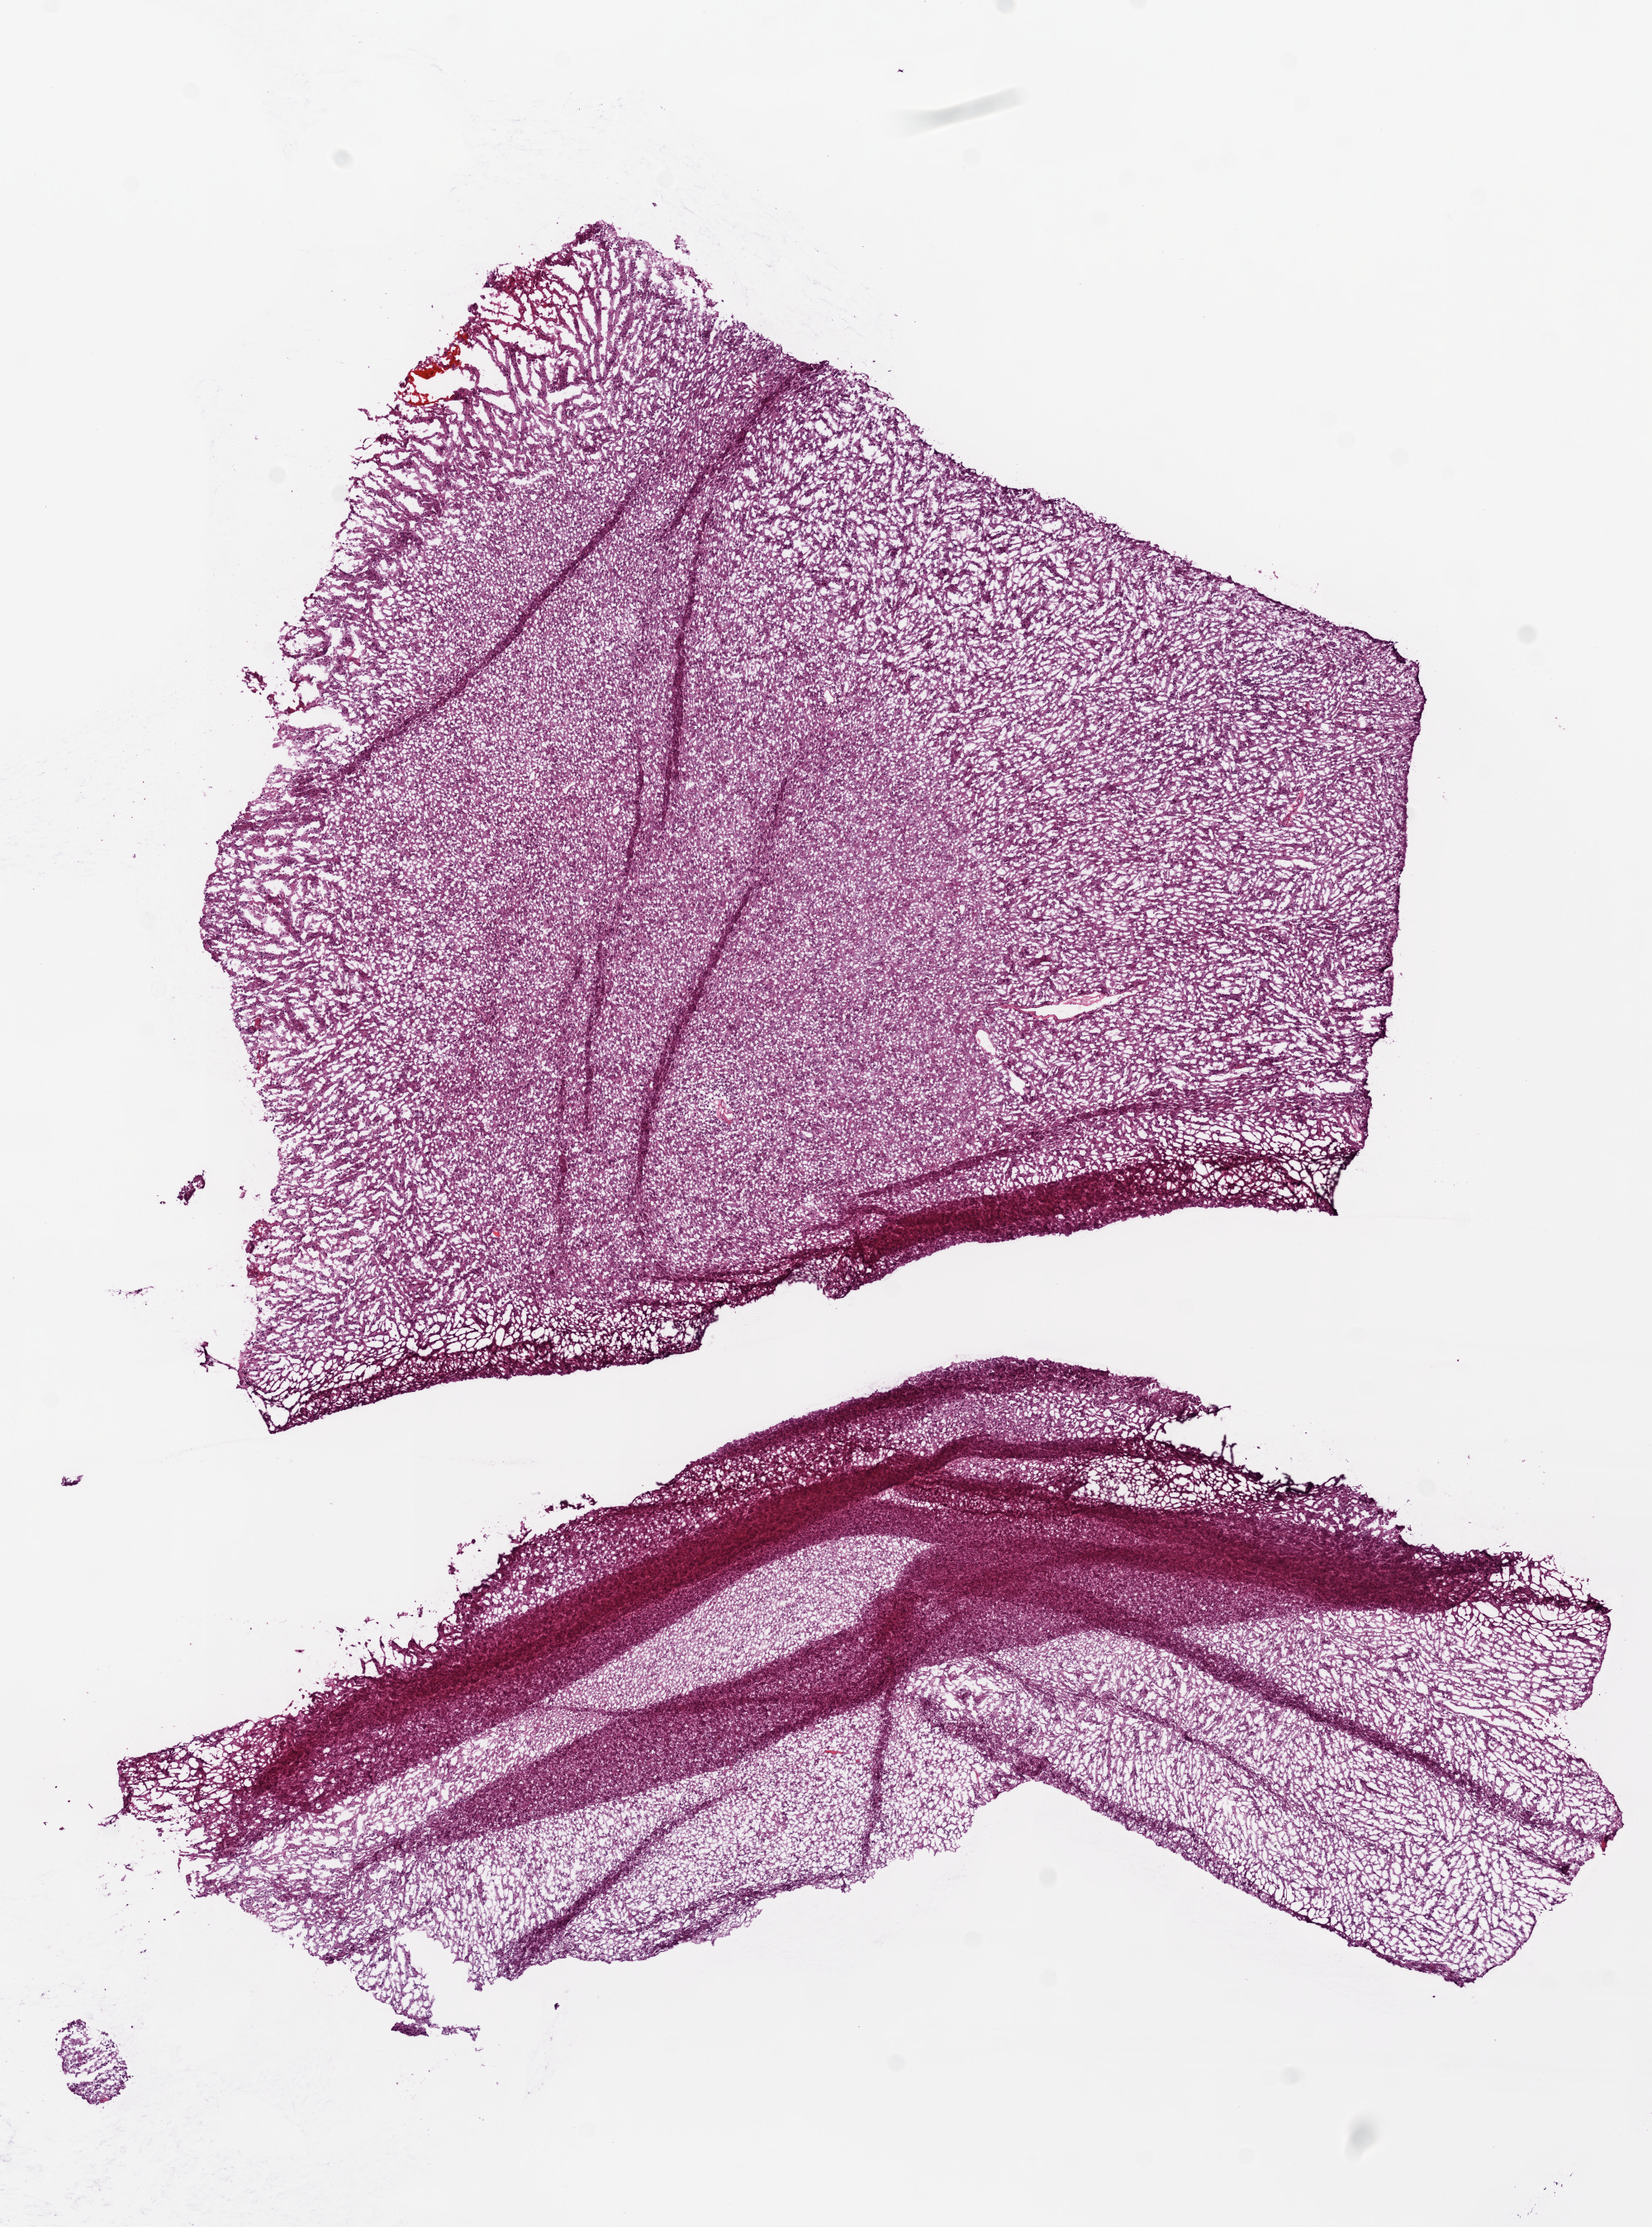
Digitized H&E-stained tissue section (whole slide), low-resolution overview of the scanned area, about 8.0 x 10.8 mm; frozen section from the top of the tissue portion; primary tumour sample from the brain. Female patient; age at initial diagnosis 64 years. Composition of this section per pathologist review: tumour cells 100%, tumour nuclei 80%, normal cells 0%, stromal cells 0%, necrosis 0%.
• histologic diagnosis: Glioblastoma